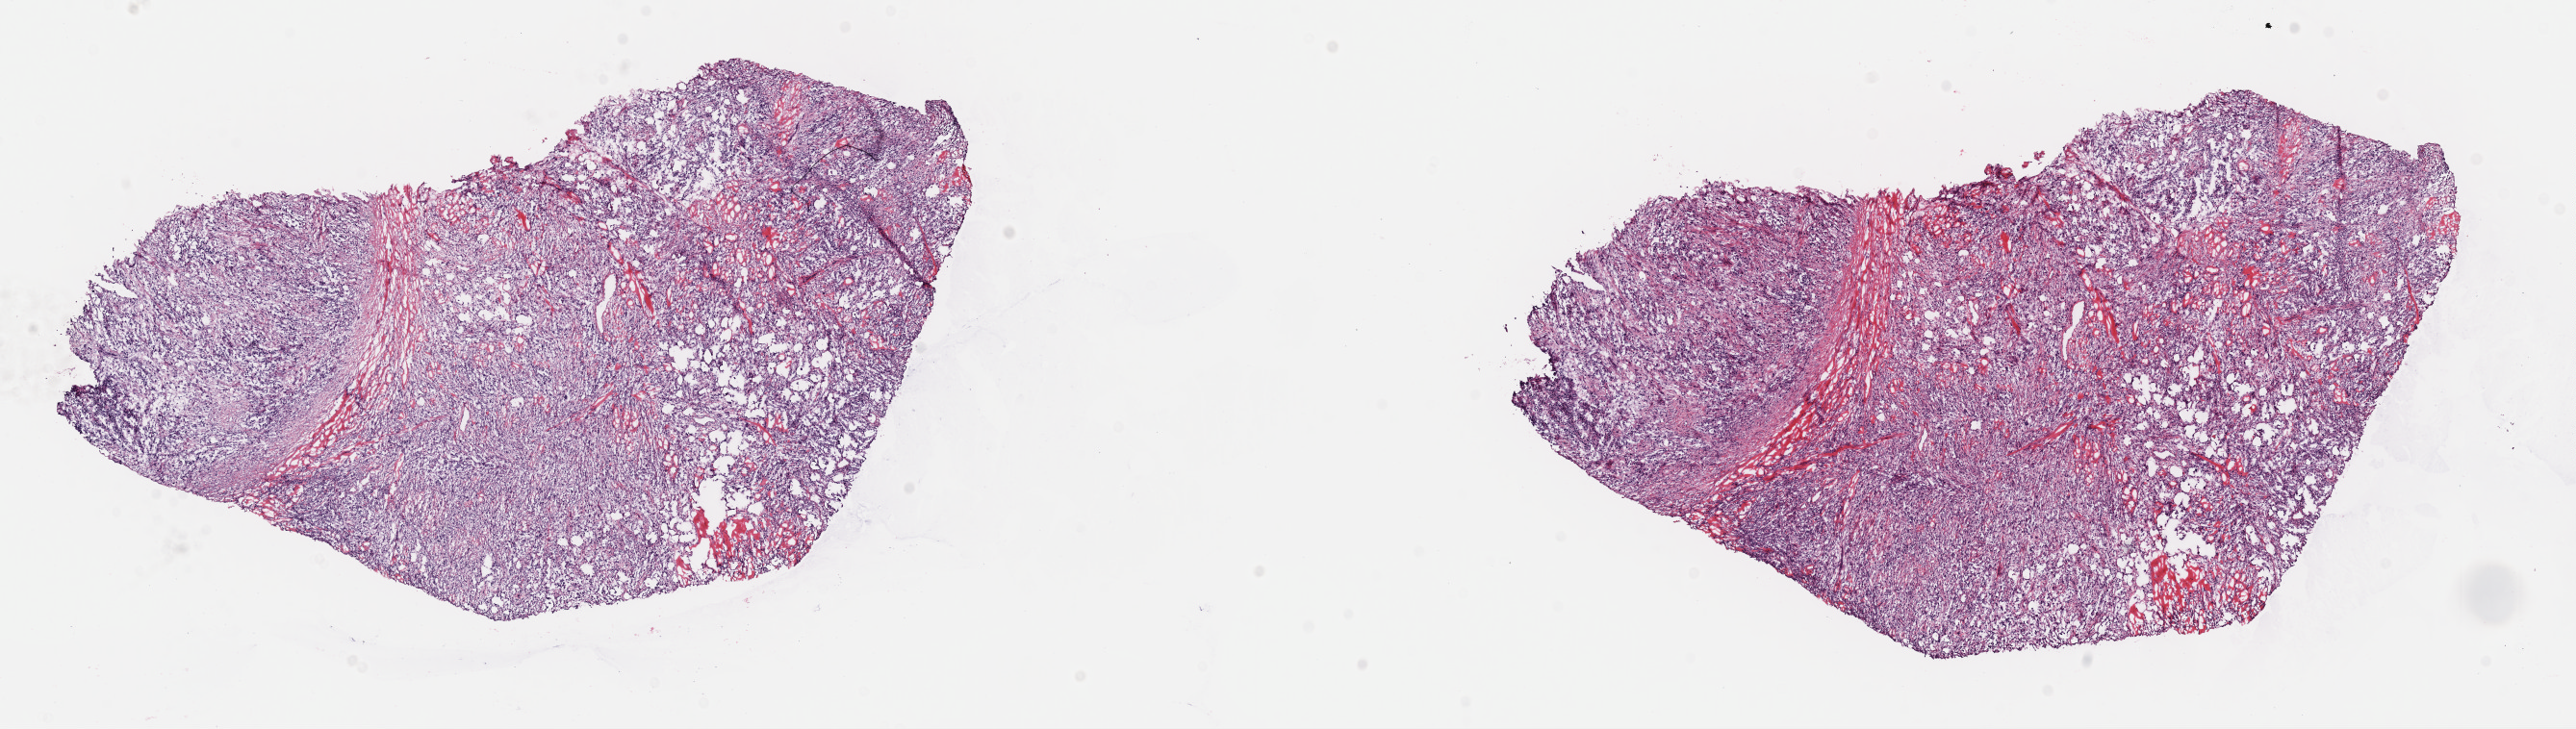
H&E-stained whole-slide image — whole scanned area (about 21.1 x 6.0 mm, slide scanned at 40x) shown as a low-resolution overview, frozen section from the top of the tissue portion, metastatic tumour sample, sampled site not recorded. Male patient; age at initial diagnosis 68 years. Slide review estimates, as recorded: tumour cells 80%, tumour nuclei 80%, normal cells 0%, stromal cells 20%, necrosis 0%. Inflammatory infiltration, as recorded: lymphocyte infiltration 5%, monocyte infiltration 0%, neutrophil infiltration 0%.
This section: metastatic tumour tissue. Patient diagnosis: Malignant melanoma, NOS.